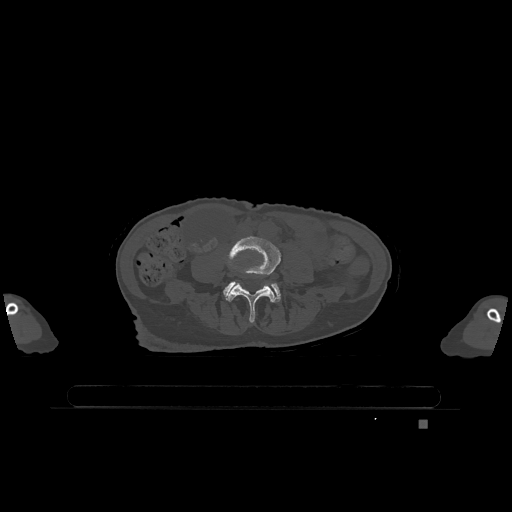
CT including the spine, one axial slice; slice 284 of 1317 in the series (ordered by position); bone window (W 1800 / L 400 HU); 0.5 mm slice thickness; 512 × 512 image matrix, field of view 500 × 500 mm. Patient: female, 74 years. From the clinical record (not read from this slice): primary cancer: lung.
Annotated regions visible in this slice (semi-automatically segmented with operator editing):
- L4 vertebra: bounding box [x1, y1, x2, y2] px = [226, 235, 280, 322]
- L5 vertebra: [223, 281, 281, 302]